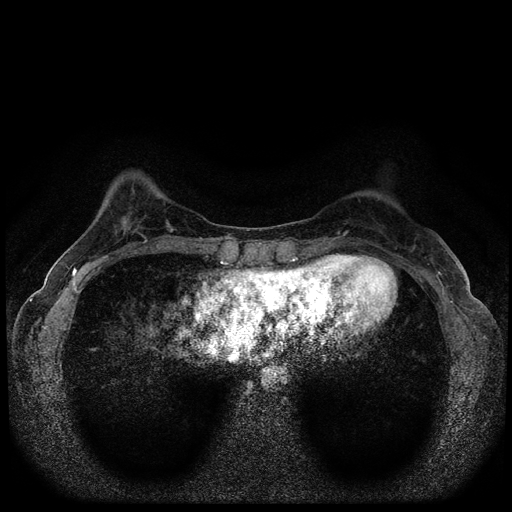
Breast MRI (dynamic contrast-enhanced, multi-phase), one axial slice. Slice 30 of 116 in the series (ordered by position). Dynamic contrast-enhanced series, time point 2 of 5 at this slice position (early post-contrast). 1.5 T. TE 2.7 ms, TR 5.6 ms. 2 mm slice thickness. 512 × 512 image matrix. Female patient, age 40 years.
Outlined on this slice (semi-automatic segmentation, software-assisted and operator-edited):
- breast lesion (labelled benign in the annotation): bounding box [x1, y1, x2, y2] px = [119, 219, 144, 237]